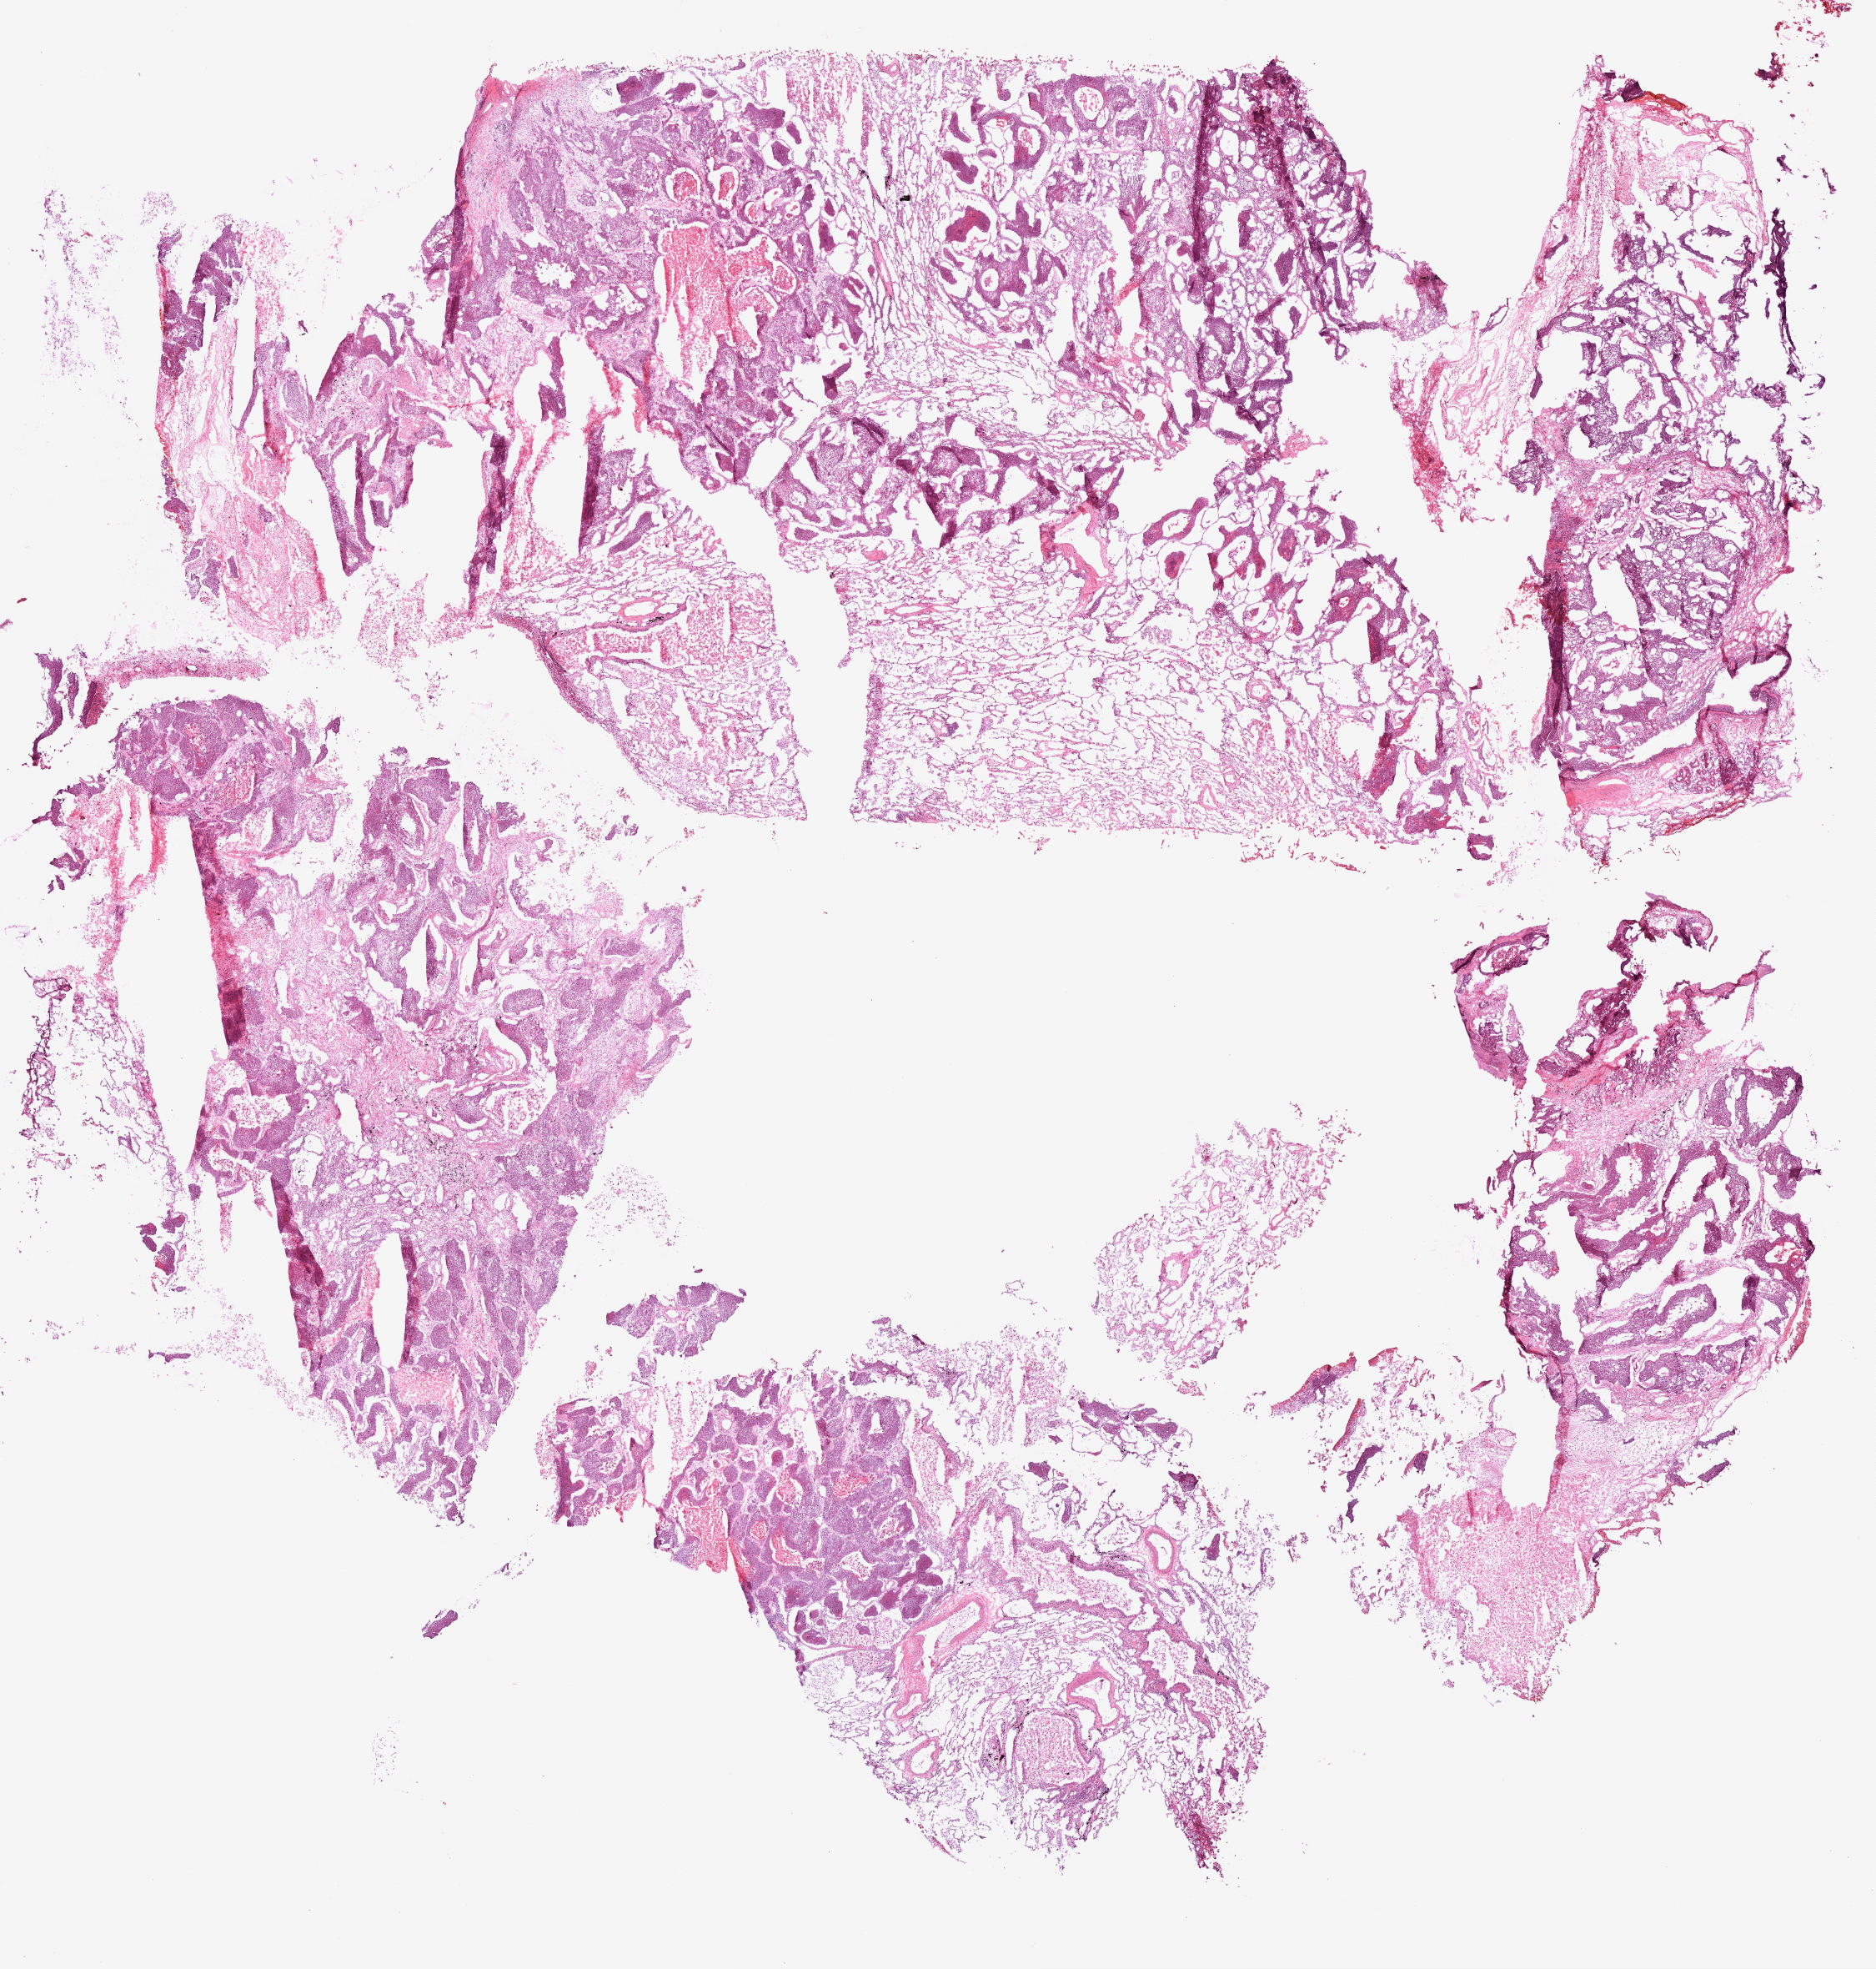
Digitized Hematoxylin and eosin (H&E) stained tissue section (whole slide) — low-resolution overview of the scanned area, about 18.1 x 18.9 mm (from a 20x scan); frozen section; primary tumour sample from the lung. Patient: male, age at initial diagnosis 73 years. Slide review estimates, as recorded: tumour cells 55%, tumour nuclei 65%.
Diagnosis: Squamous cell carcinoma, NOS.